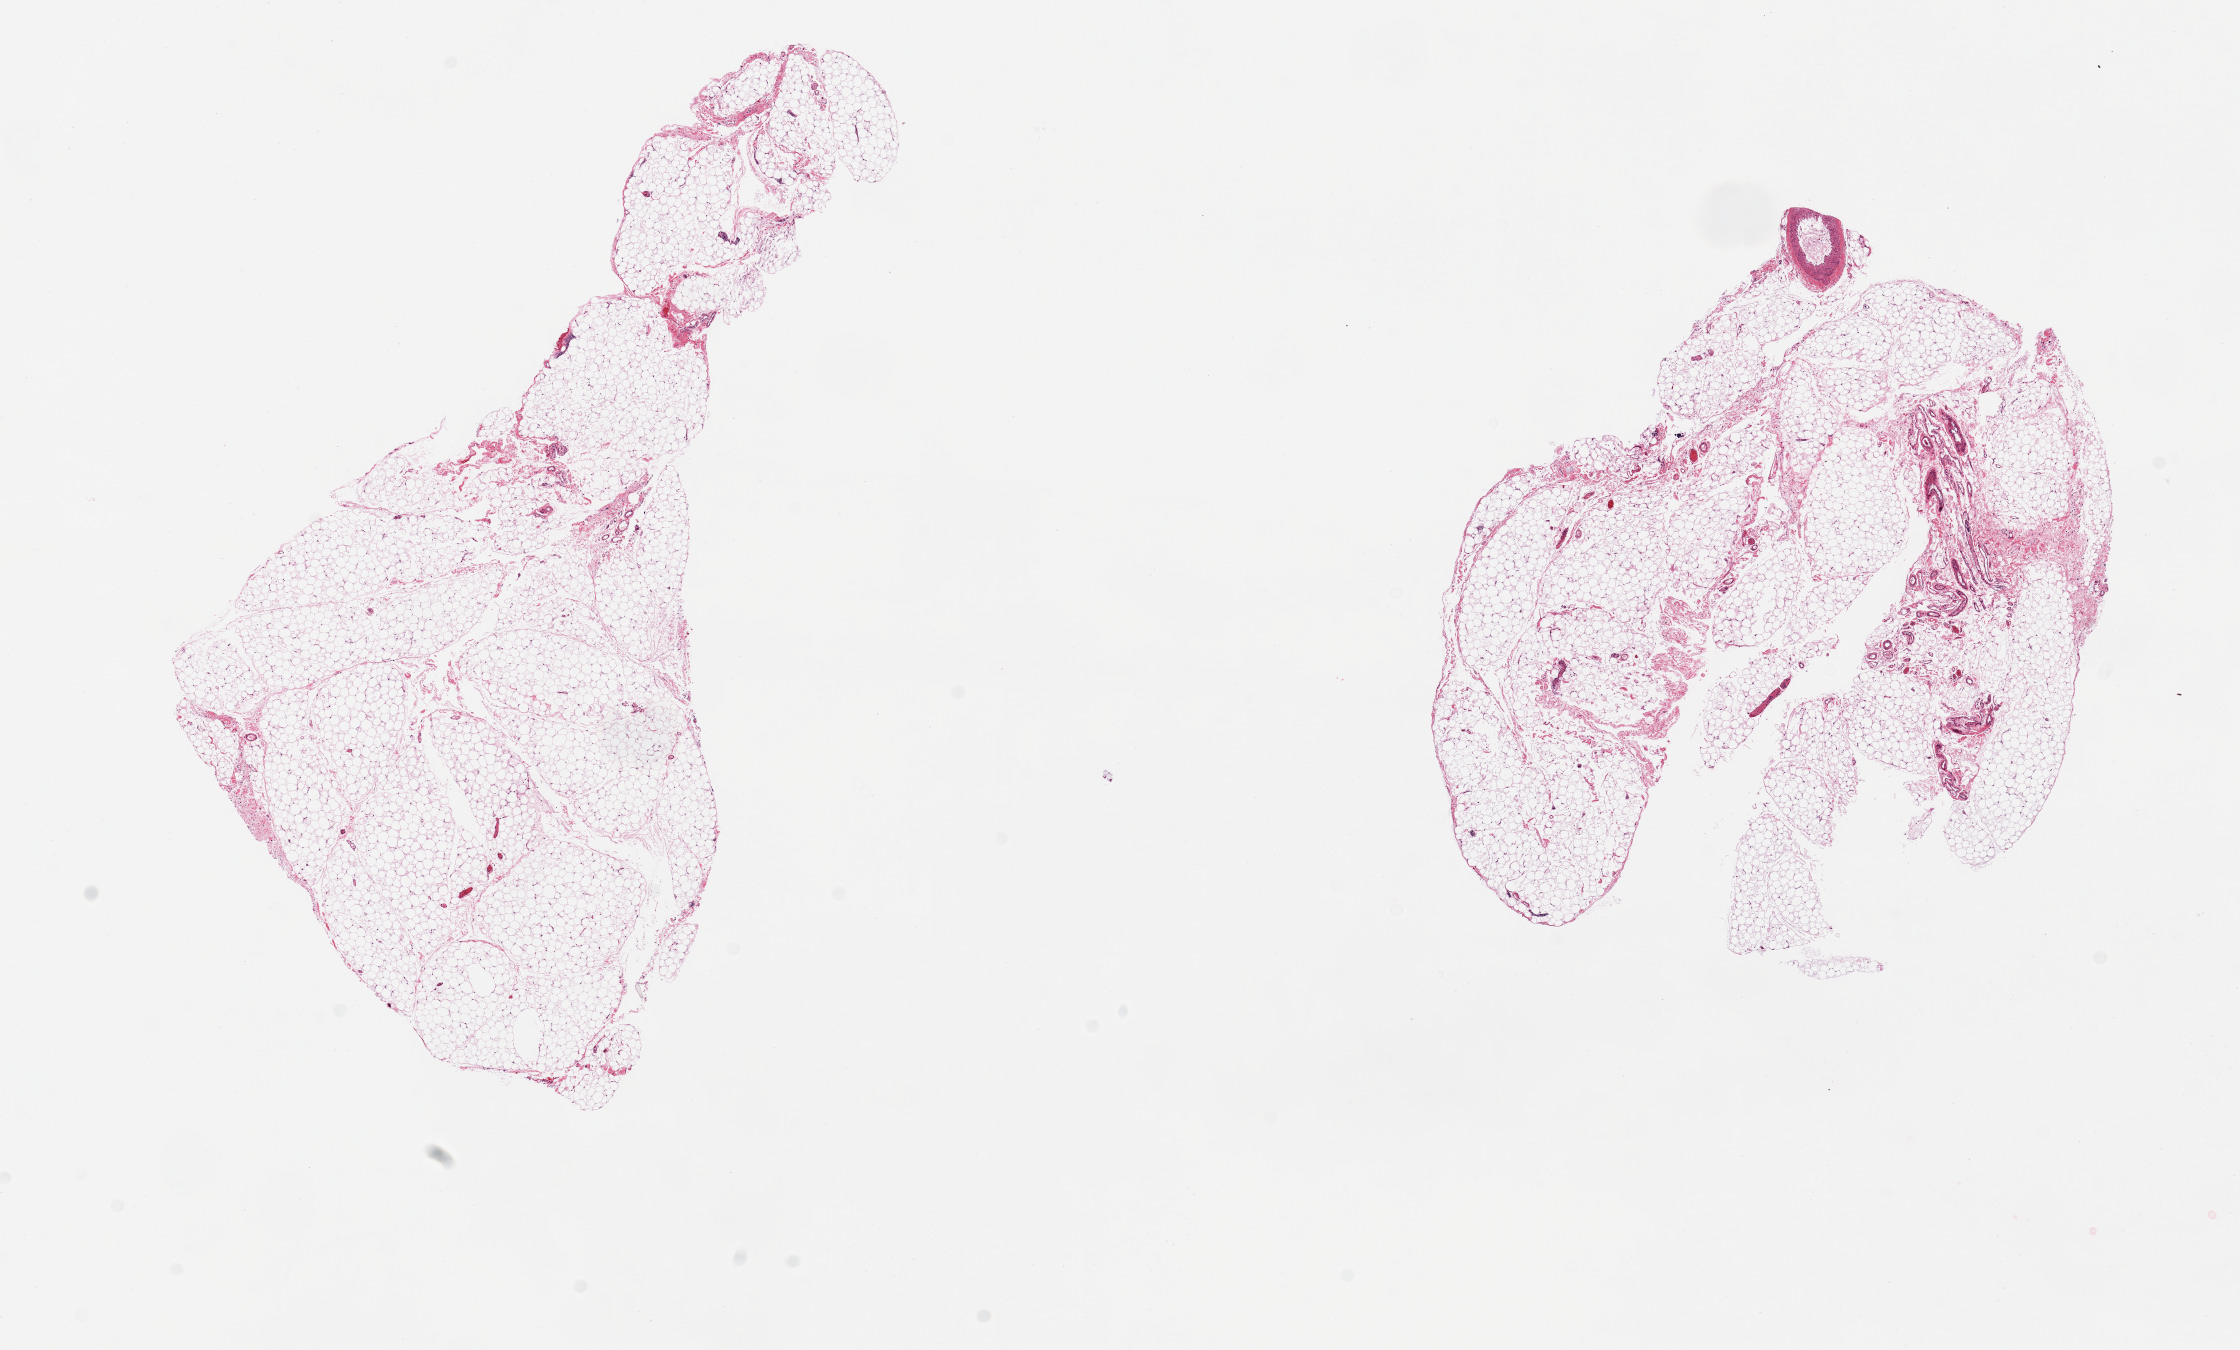
Whole-slide image, haematoxylin and eosin stain, brightfield — low-resolution overview of the scanned area, about 17.7 x 10.7 mm; PAXgene-fixed, paraffin-embedded tissue; sampled site (target tissue): omentum; tissue donor sample. Donor sex: female.
• review note (as recorded): 2 pieces